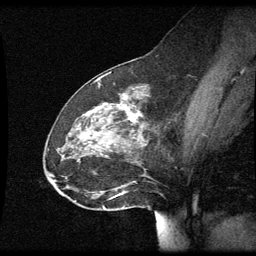
Breast MRI (dynamic contrast-enhanced), one sagittal slice. Slice 26 of 60 in the series (ordered by position). Dynamic contrast-enhanced series, image 2 of 3 at this slice position (ordered by acquisition). 1.5 T. TE 4.2 ms, TR 8.9 ms. 256 × 256 image matrix. Patient: female, 49 years. From the clinical record (not read from this slice): setting: breast cancer imaged before/during neoadjuvant chemotherapy; receptor status: HR-positive, HER2-negative.
Annotated regions visible in this slice (semi-automatically segmented with operator editing):
- analysis volume of interest (the breast-tissue region the enhancement analysis was run in; not a lesion): bounding box (x1, y1, x2, y2) in pixels: (46, 92, 153, 205)
- tumour enhancement mask (voxels above the 70 % enhancement threshold inside the analysis volume of interest): (128, 114, 141, 123)